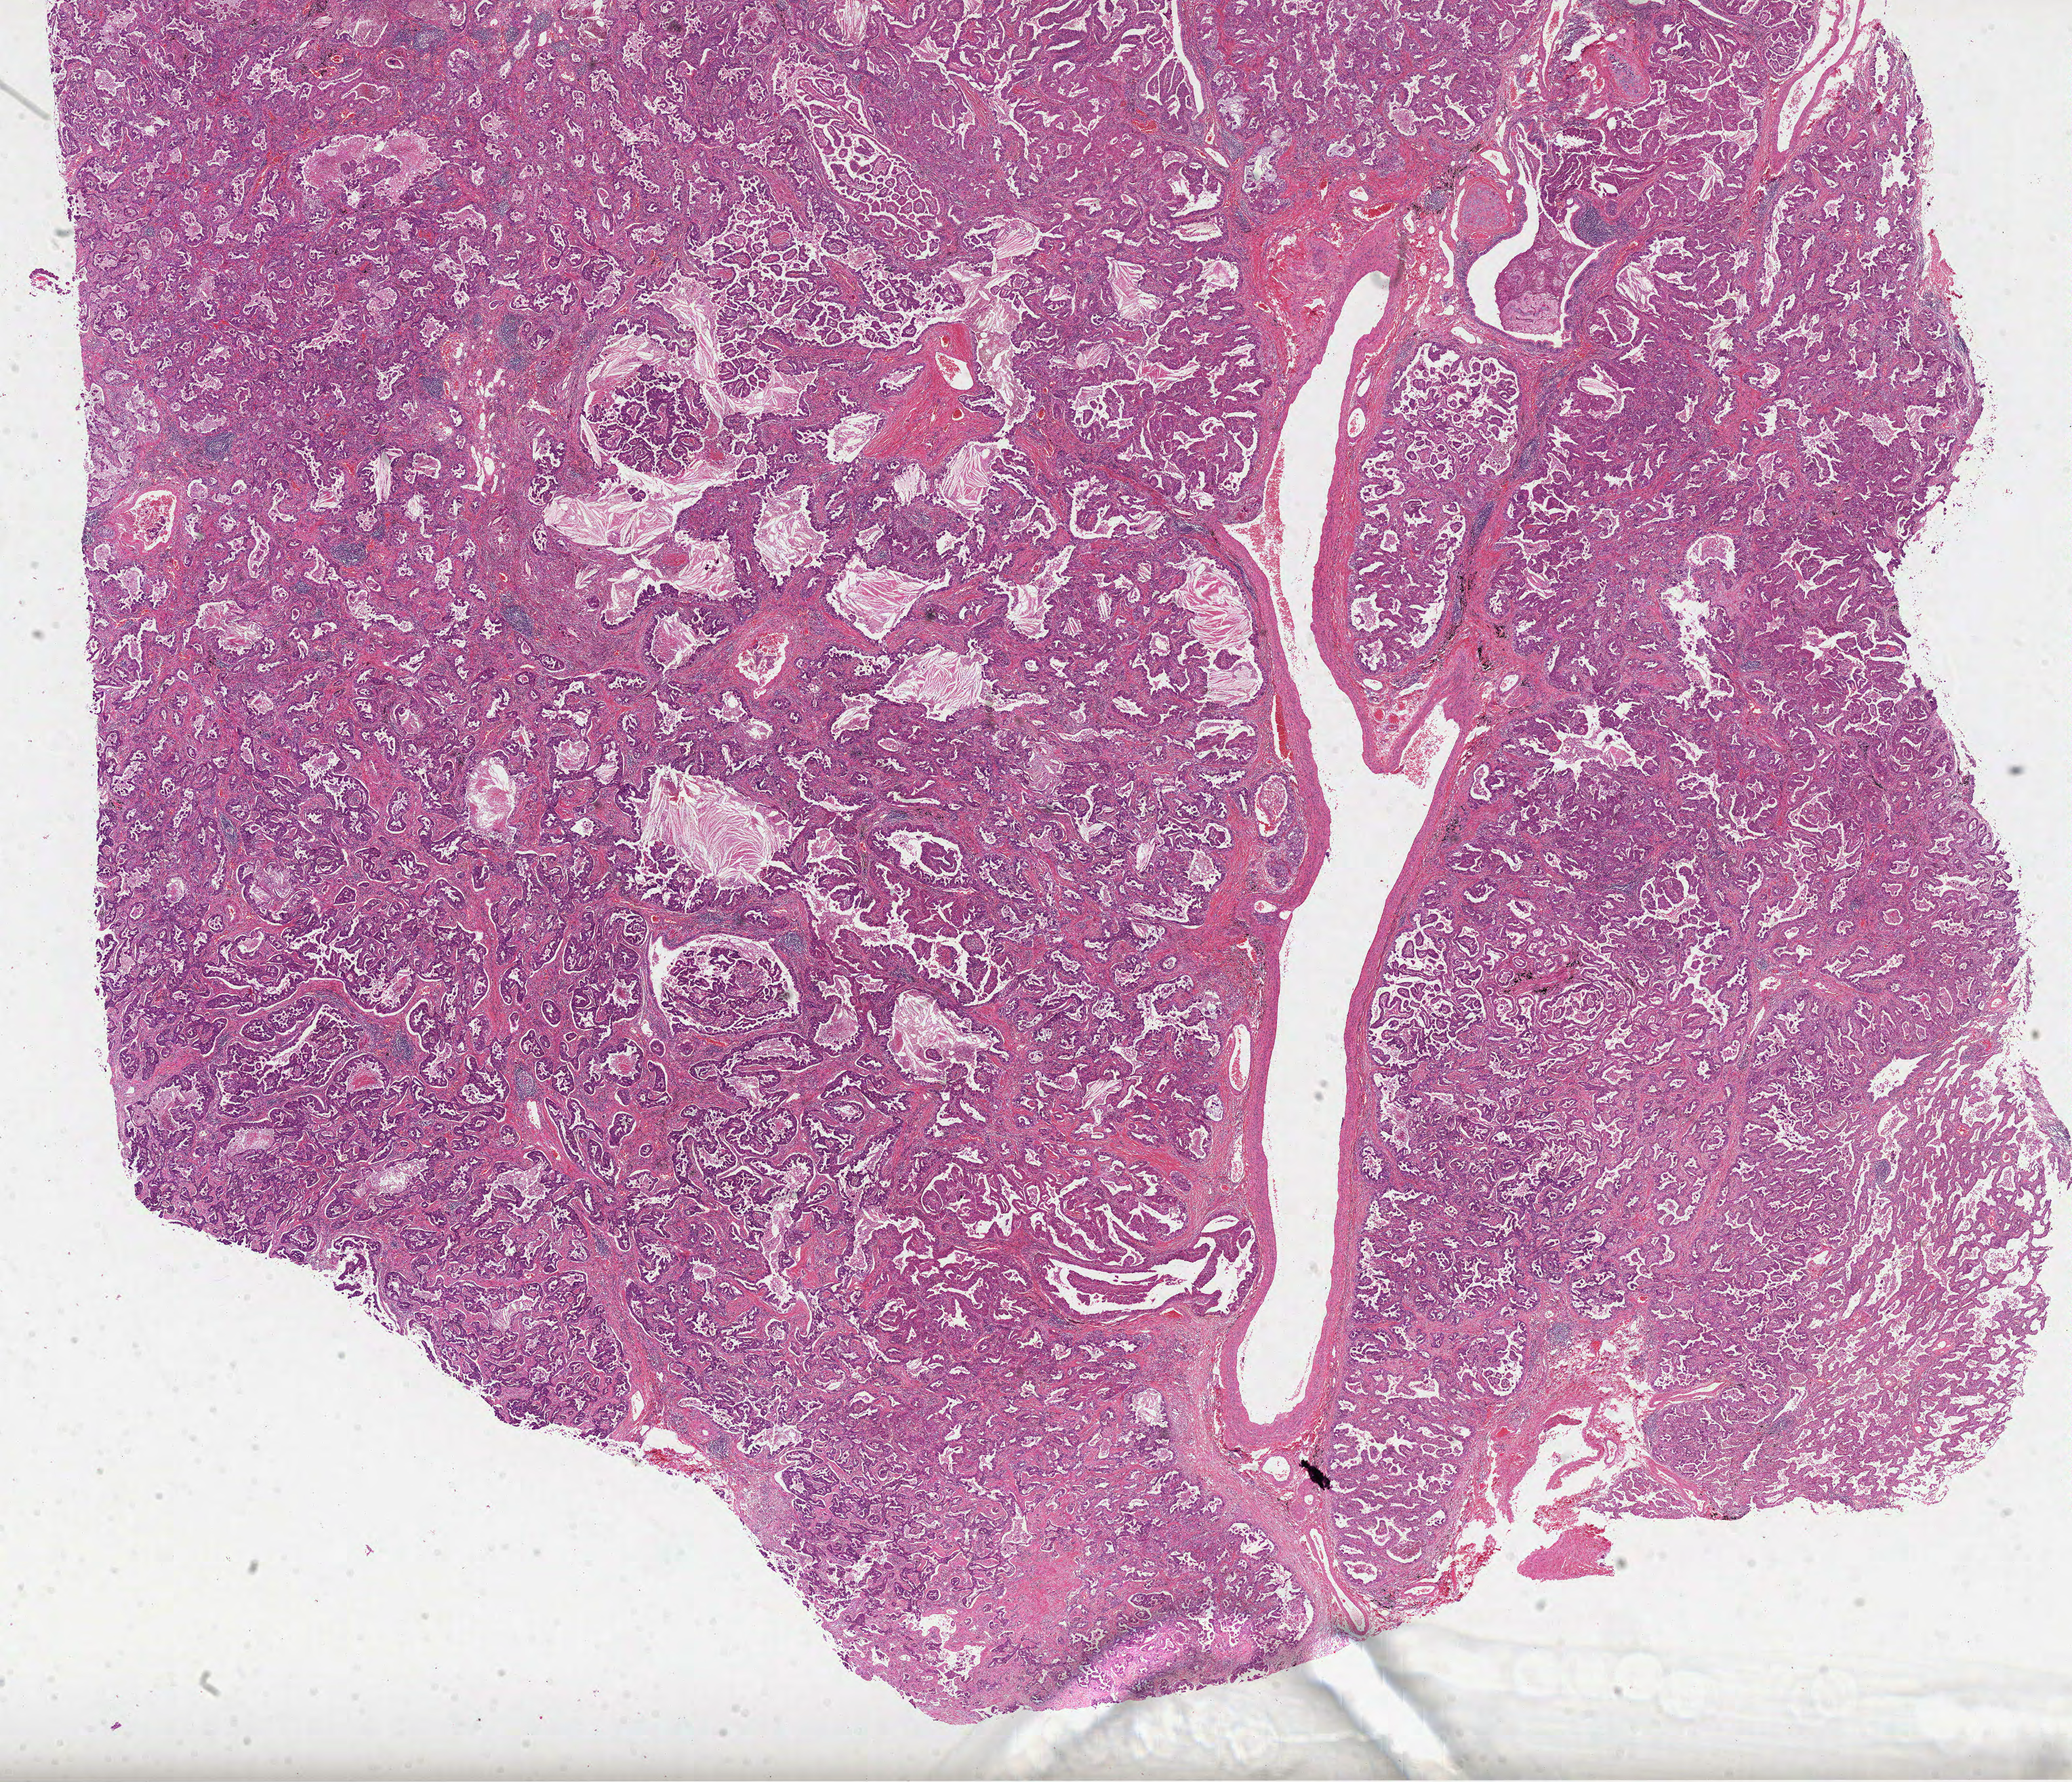
H&E-stained whole-slide image, low-resolution overview of the scanned area, about 24.7 x 21.2 mm (slide scanned at 40x); FFPE section; lung, primary tumour sample. Patient: female, age at initial diagnosis 65 years.
Histologic diagnosis: Adenocarcinoma with mixed subtypes (overlapping lesion of lung). AJCC pathologic stage: IB (6th edition). Laterality: right.